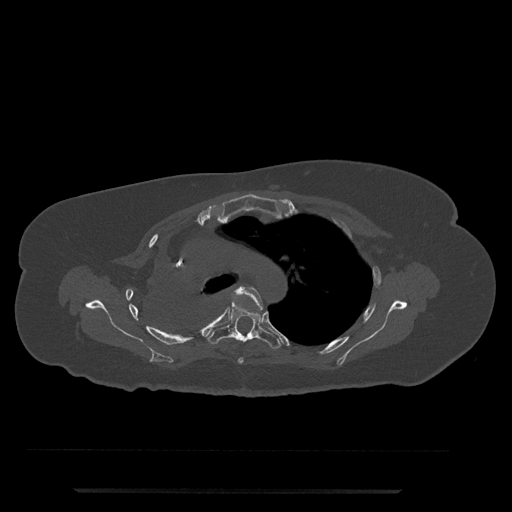
CT including the spine, one axial slice. Position 557 of 797 along the scan axis. Reconstruction kernel Br40s/3. 120 kVp. Bone window (W 1800 / L 400 HU). 0.5 mm slice thickness. 512 × 512 image matrix. Female patient, age 51 years. Case-level facts recorded for this patient, not image findings: primary cancer: neuro; vertebrae with lytic lesions (as recorded): T8.
Outlined on this slice (semi-automatically segmented with operator editing):
- T4 vertebra: bounding box (x1, y1, x2, y2) in pixels: (234, 286, 263, 364)
- T5 vertebra: (207, 301, 282, 349)